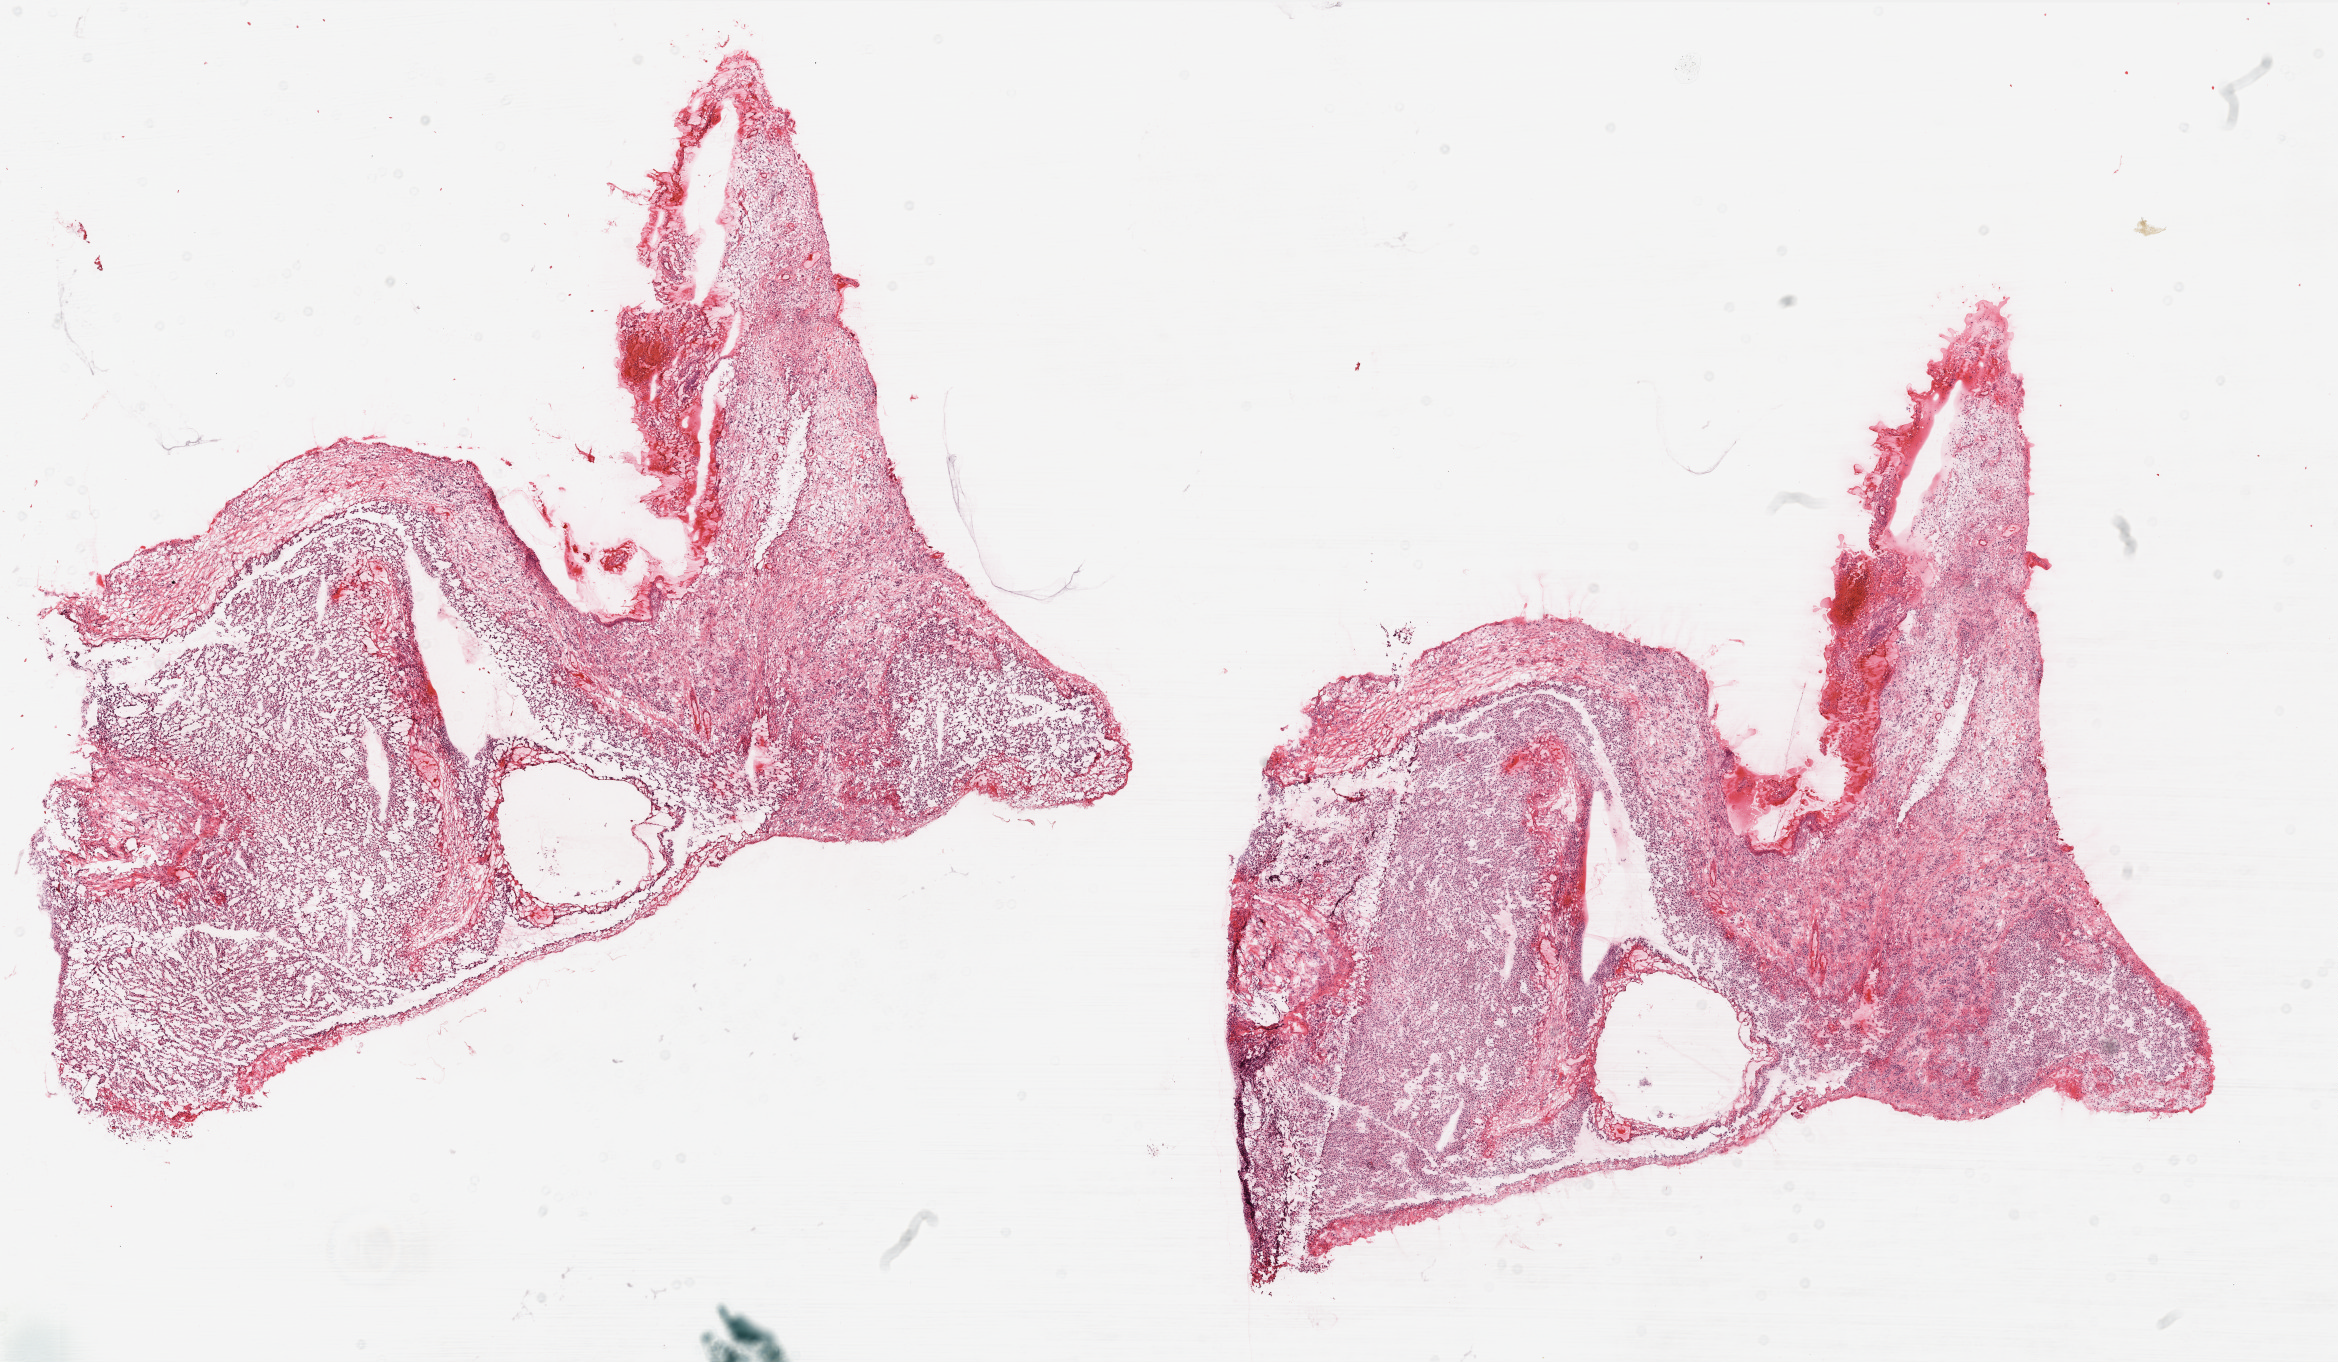
Hematoxylin and eosin (H&E) stained whole-slide image — low-resolution overview of the scanned area, about 18.8 x 11.0 mm (from a 20x scan). Frozen section from the top of the tissue portion. Sample: primary tumour, brain. Female, age 31 years at initial diagnosis. Slide review estimates, as recorded: tumour cells 75%, tumour nuclei 95%, normal cells 0%, stromal cells 25%, necrosis 0%.
Pathologic diagnosis: Glioblastoma.